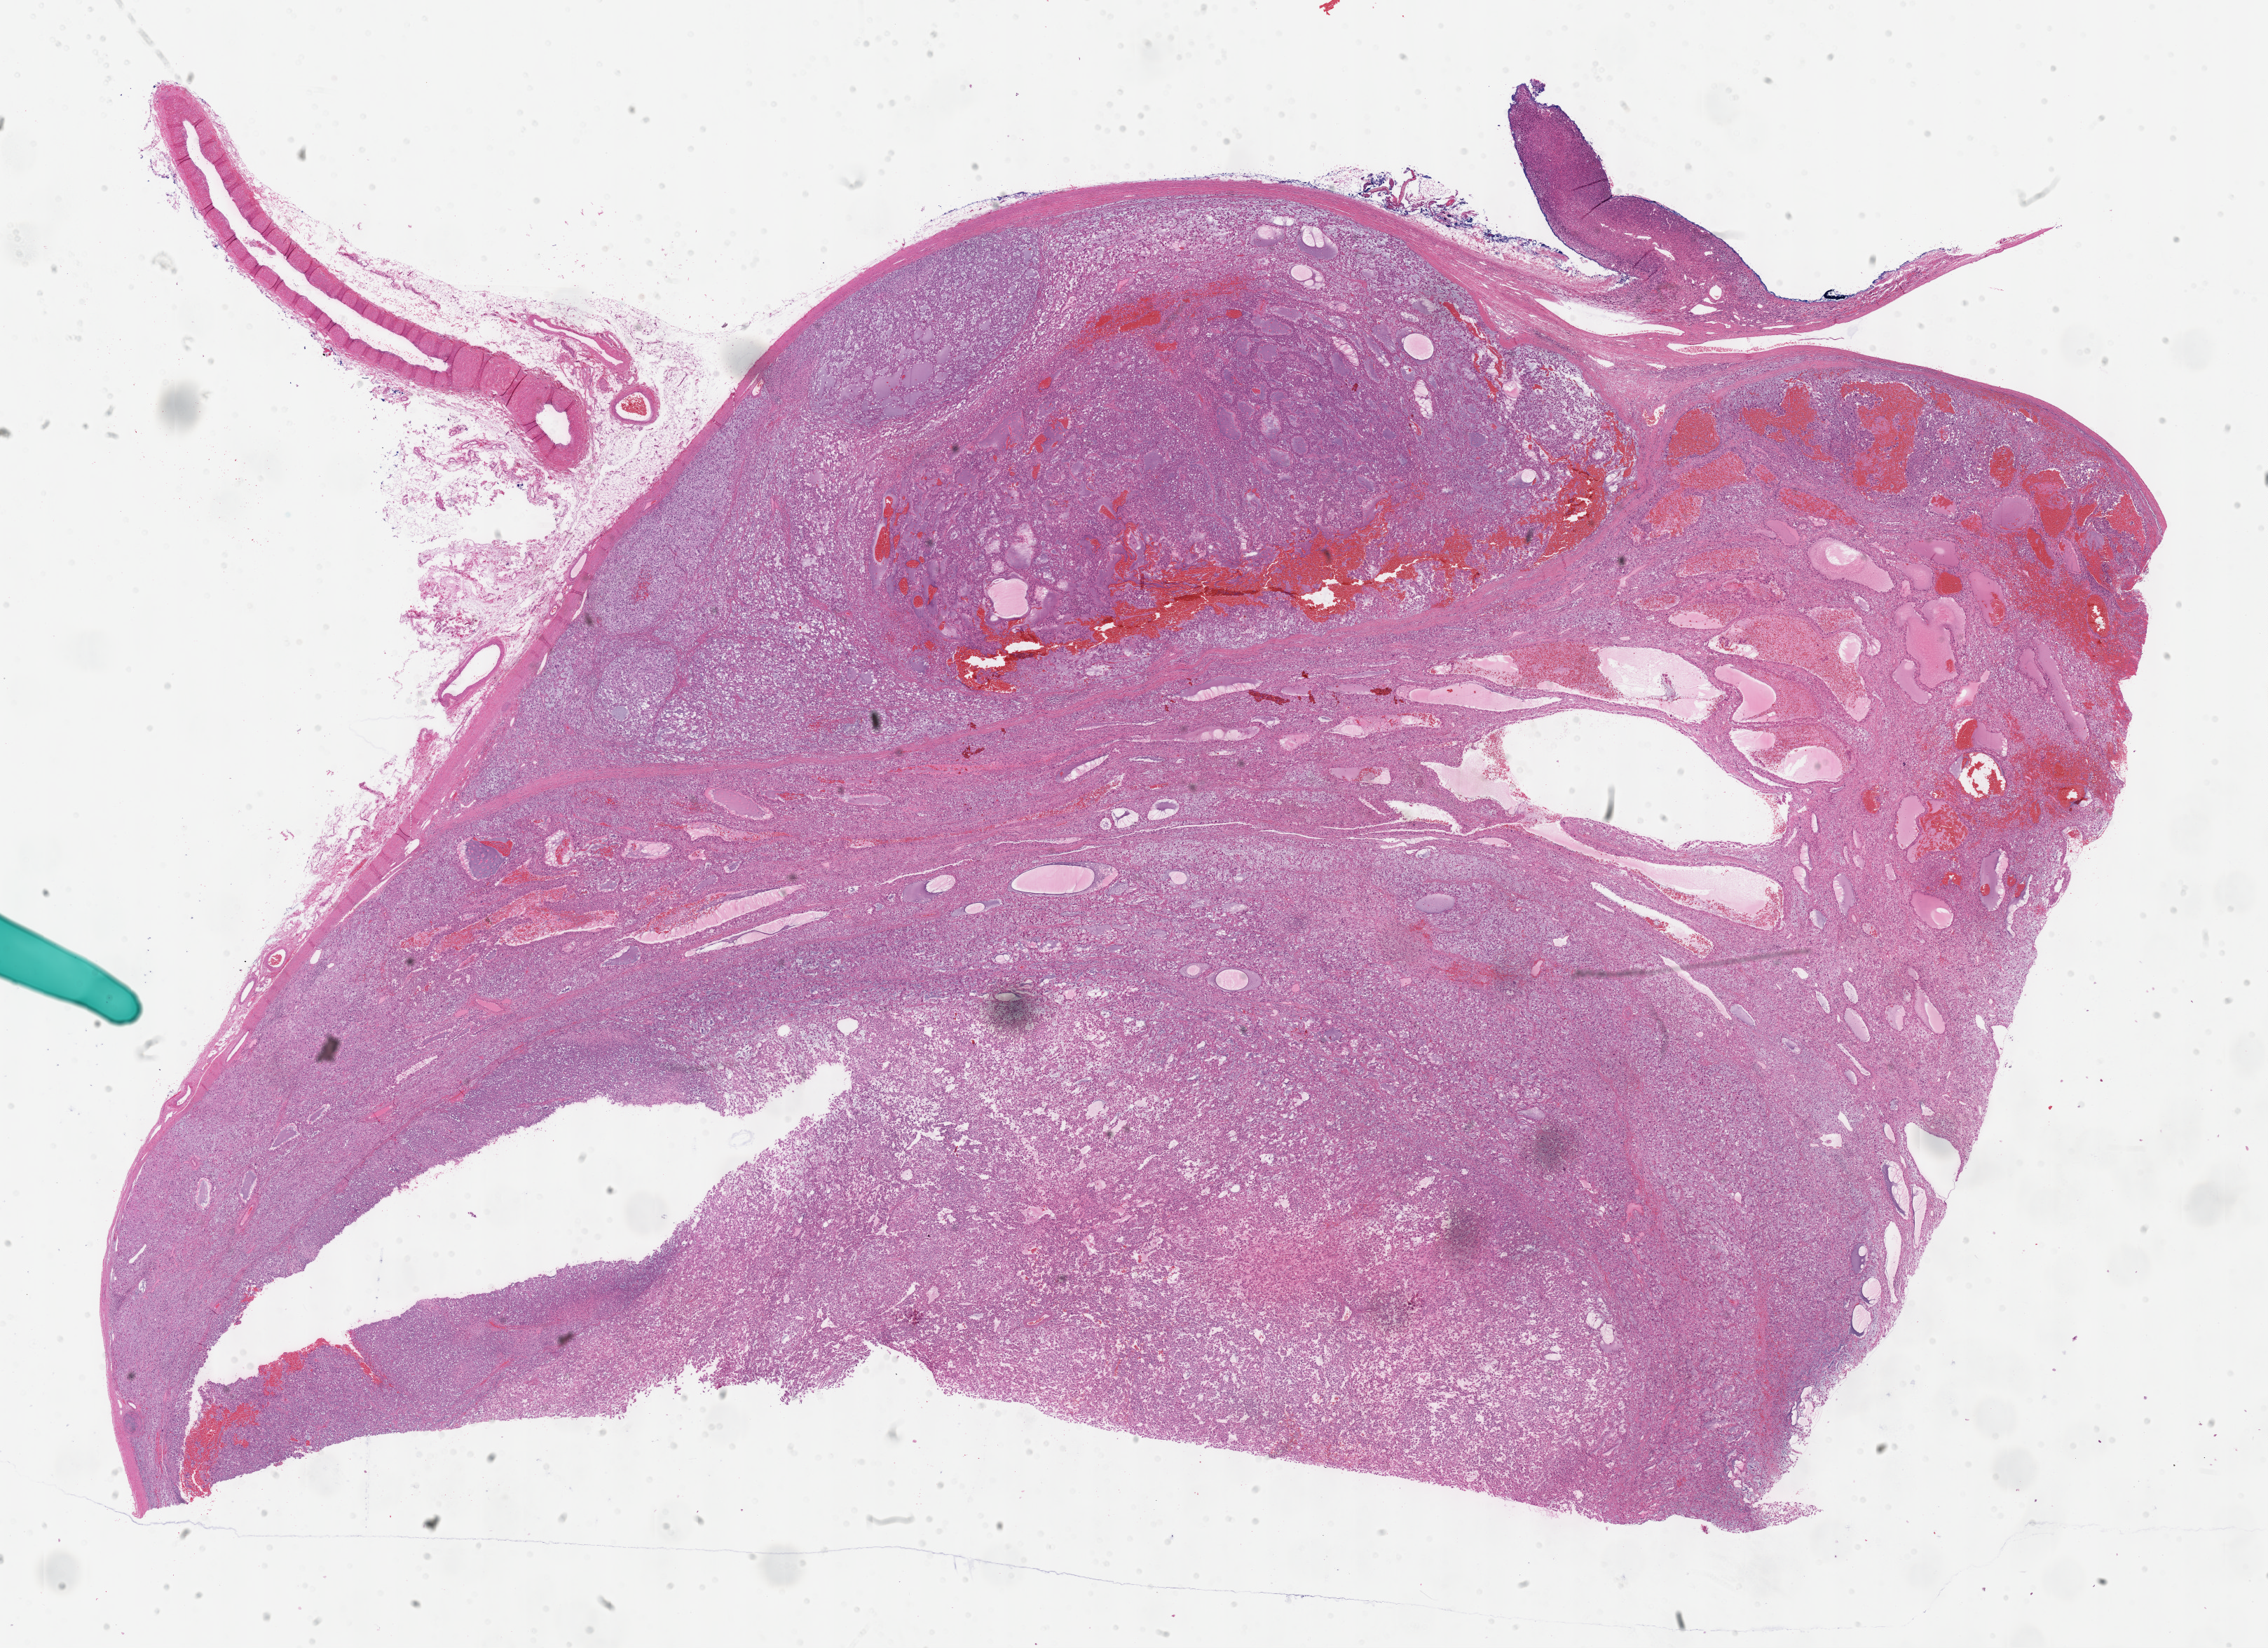
Hematoxylin and eosin (H&E) stained whole-slide image, low-resolution overview of the scanned area, about 26.2 x 19.0 mm (from a 40x scan), formalin-fixed paraffin-embedded (FFPE) diagnostic section, sample: primary tumour, adrenal cortex. Female patient; age at initial diagnosis 26 years.
* diagnosis: Adrenal cortical carcinoma (cortex of adrenal gland)